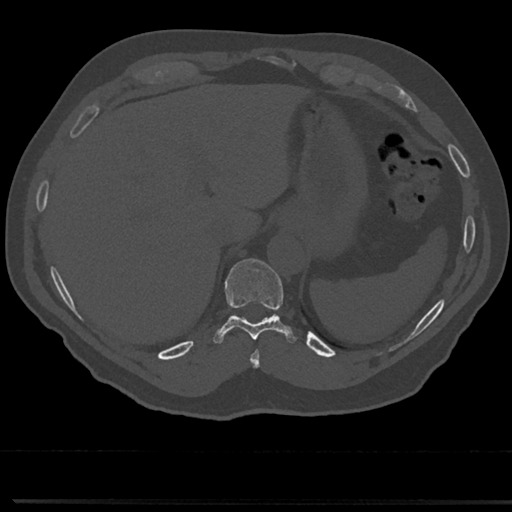
CT including the spine, one axial slice. Slice 255 of 817 in the series (ordered by position). Reconstruction kernel Br40s/3. 120 kVp. Bone window (W 1800 / L 400 HU). 0.5 mm slice thickness. 512 × 512 image matrix, field of view 355 × 355 mm. Patient: male, 61 years. From the clinical record (not read from this slice): primary cancer: prostate.
Annotated regions visible in this slice (semi-automatically segmented with operator editing):
- T10 vertebra: bounding box <209,259,299,345> (left, top, right, bottom; pixels)
- T9 vertebra: <251,342,260,368>